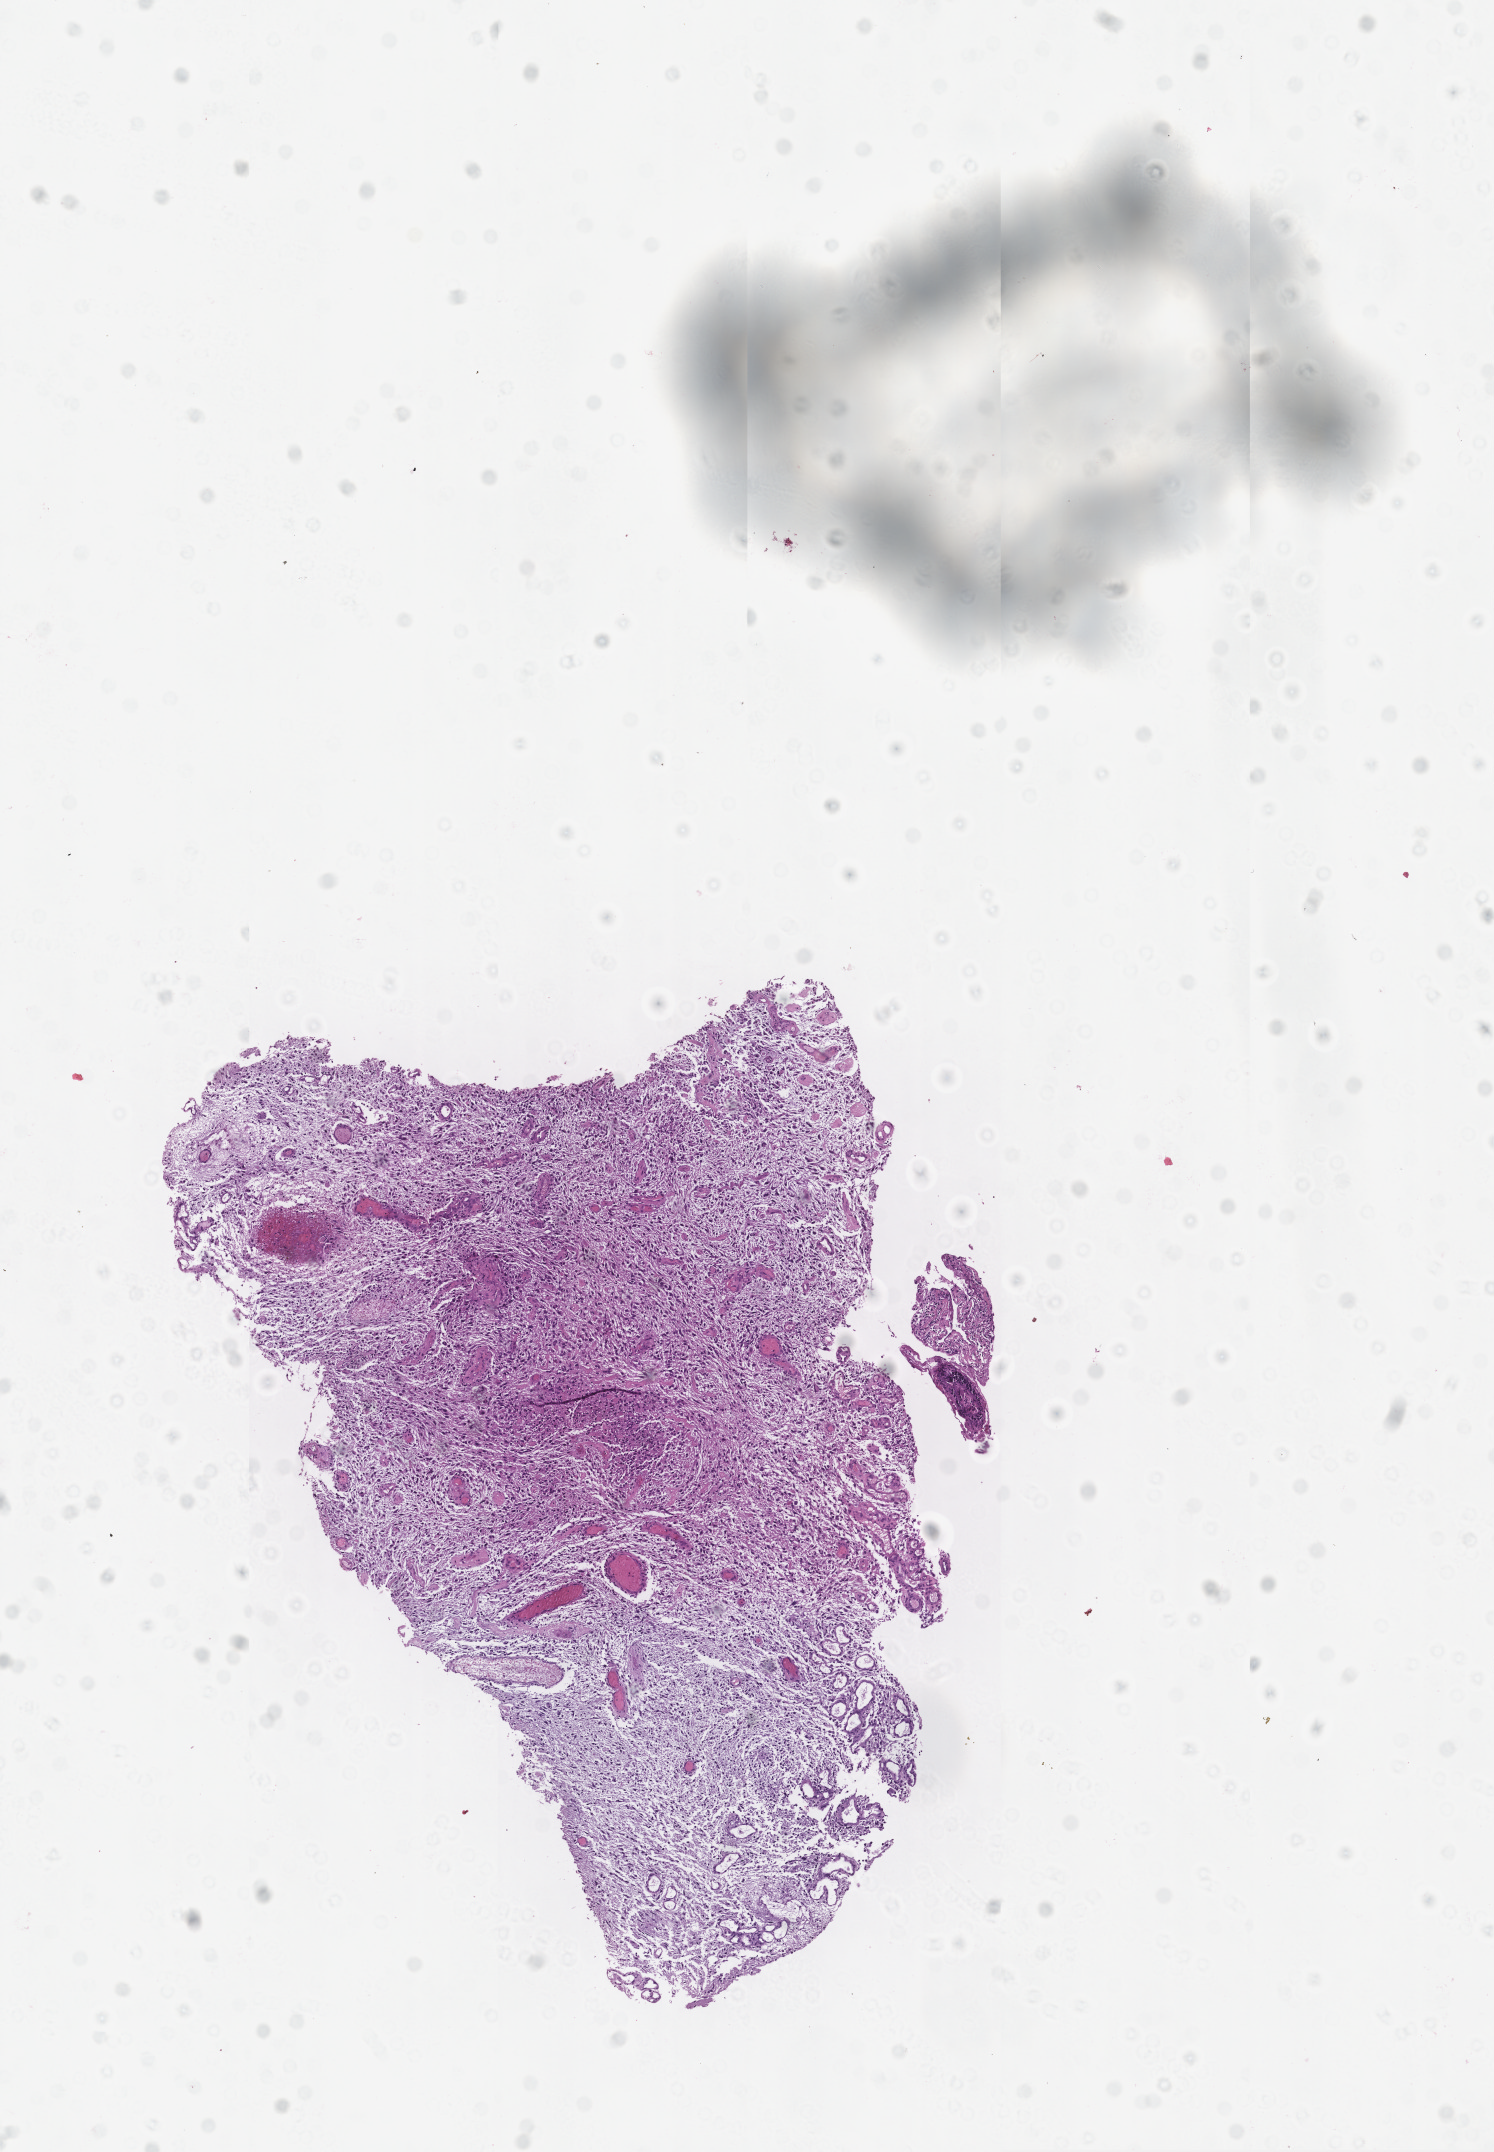
Whole-slide histology image, H&E, low-resolution overview of the scanned area, about 6.0 x 8.7 mm; brain, tumour tissue. Female, 48 y/o.
Primary tumour site (as recorded): temporal lobe. Histologic diagnosis: Glioblastoma.